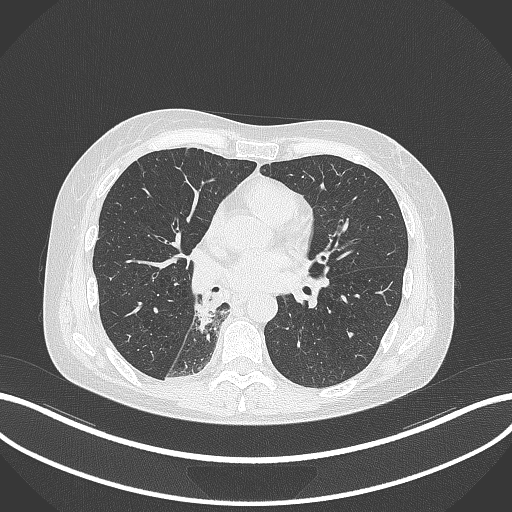
Chest CT, one axial slice; reconstruction kernel B70f; 120 kVp; lung window (W 1500 / L -600 HU); 512 × 512 image matrix, field of view 400 × 400 mm. Female patient, age 63 years. Case-level facts recorded for this patient, not image findings: clinical TNM (as recorded): T1c N0 M0.
Annotated regions visible in this slice (rectangle marked by the reading radiologist):
- lung tumour (recorded histology: adenocarcinoma): box from (x=193, y=281) to (x=222, y=336) px